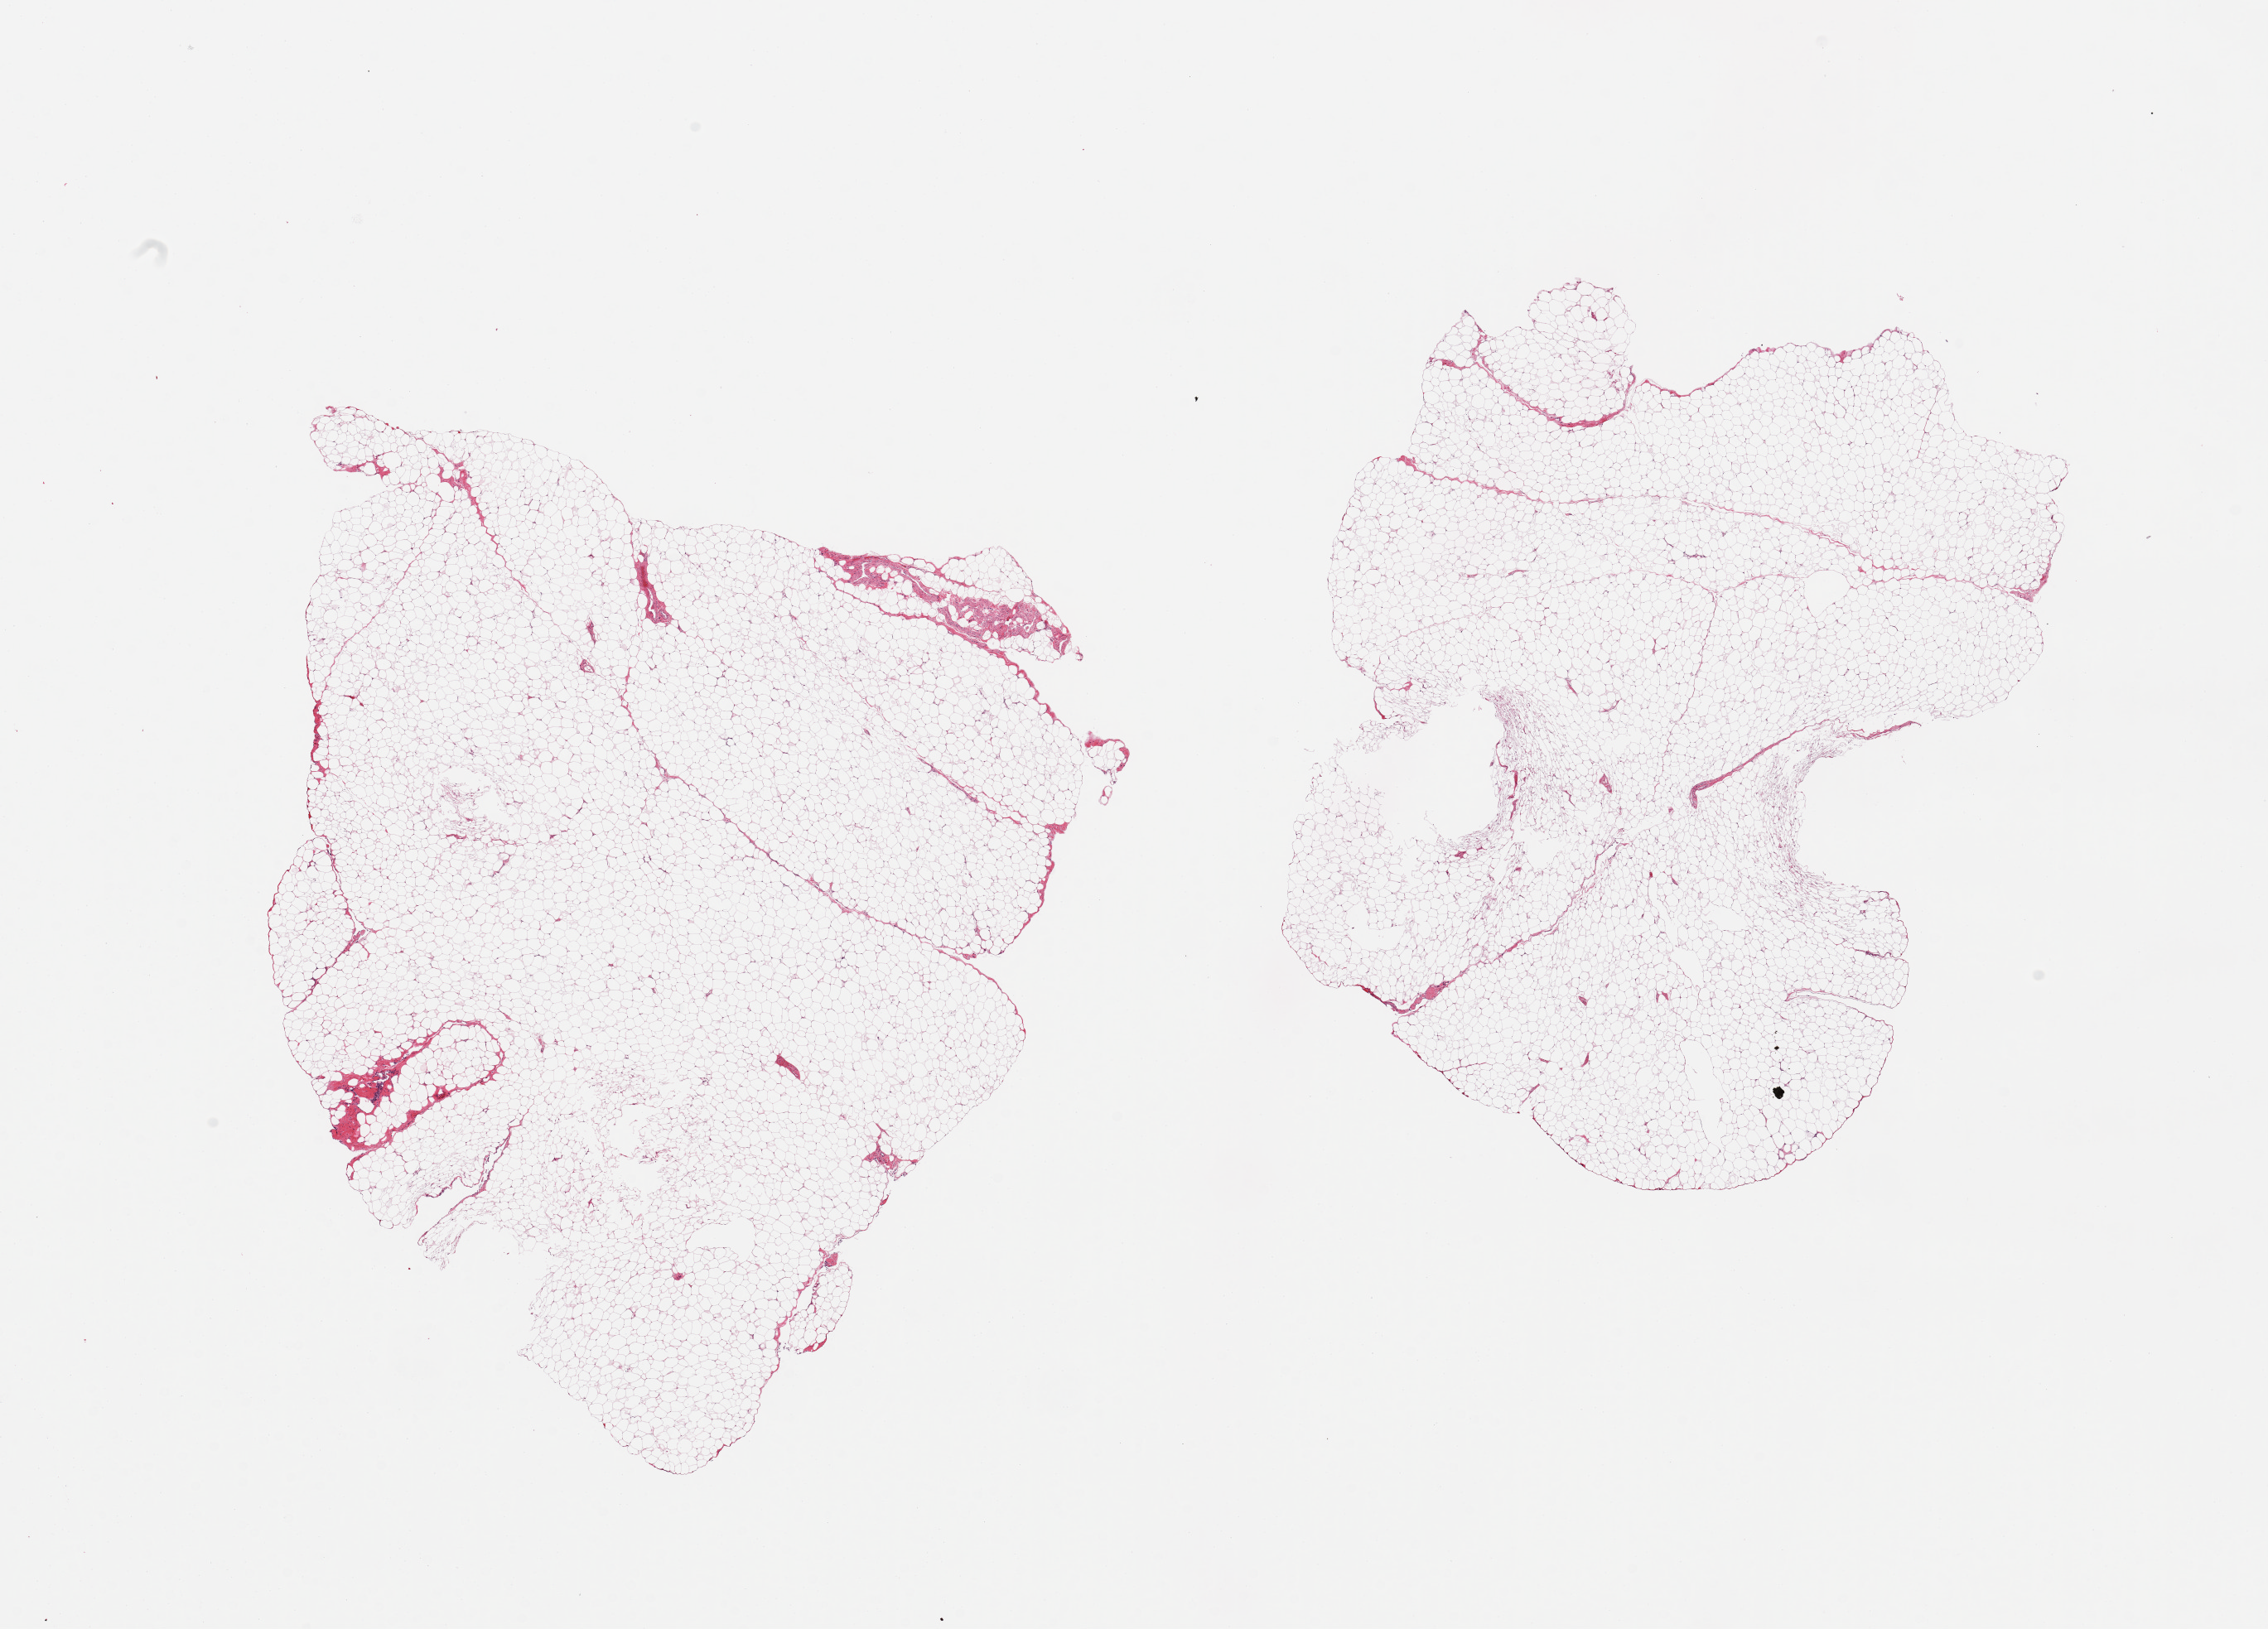
Digitized hematoxylin and eosin (H&E)-stained section — low-resolution overview of the scanned area, about 21.7 x 15.6 mm; PAXgene-fixed, paraffin-embedded tissue; target tissue: omentum; tissue donor sample. Donor: male.
Review note (as recorded): 2 pieces; mature adipose tissue.